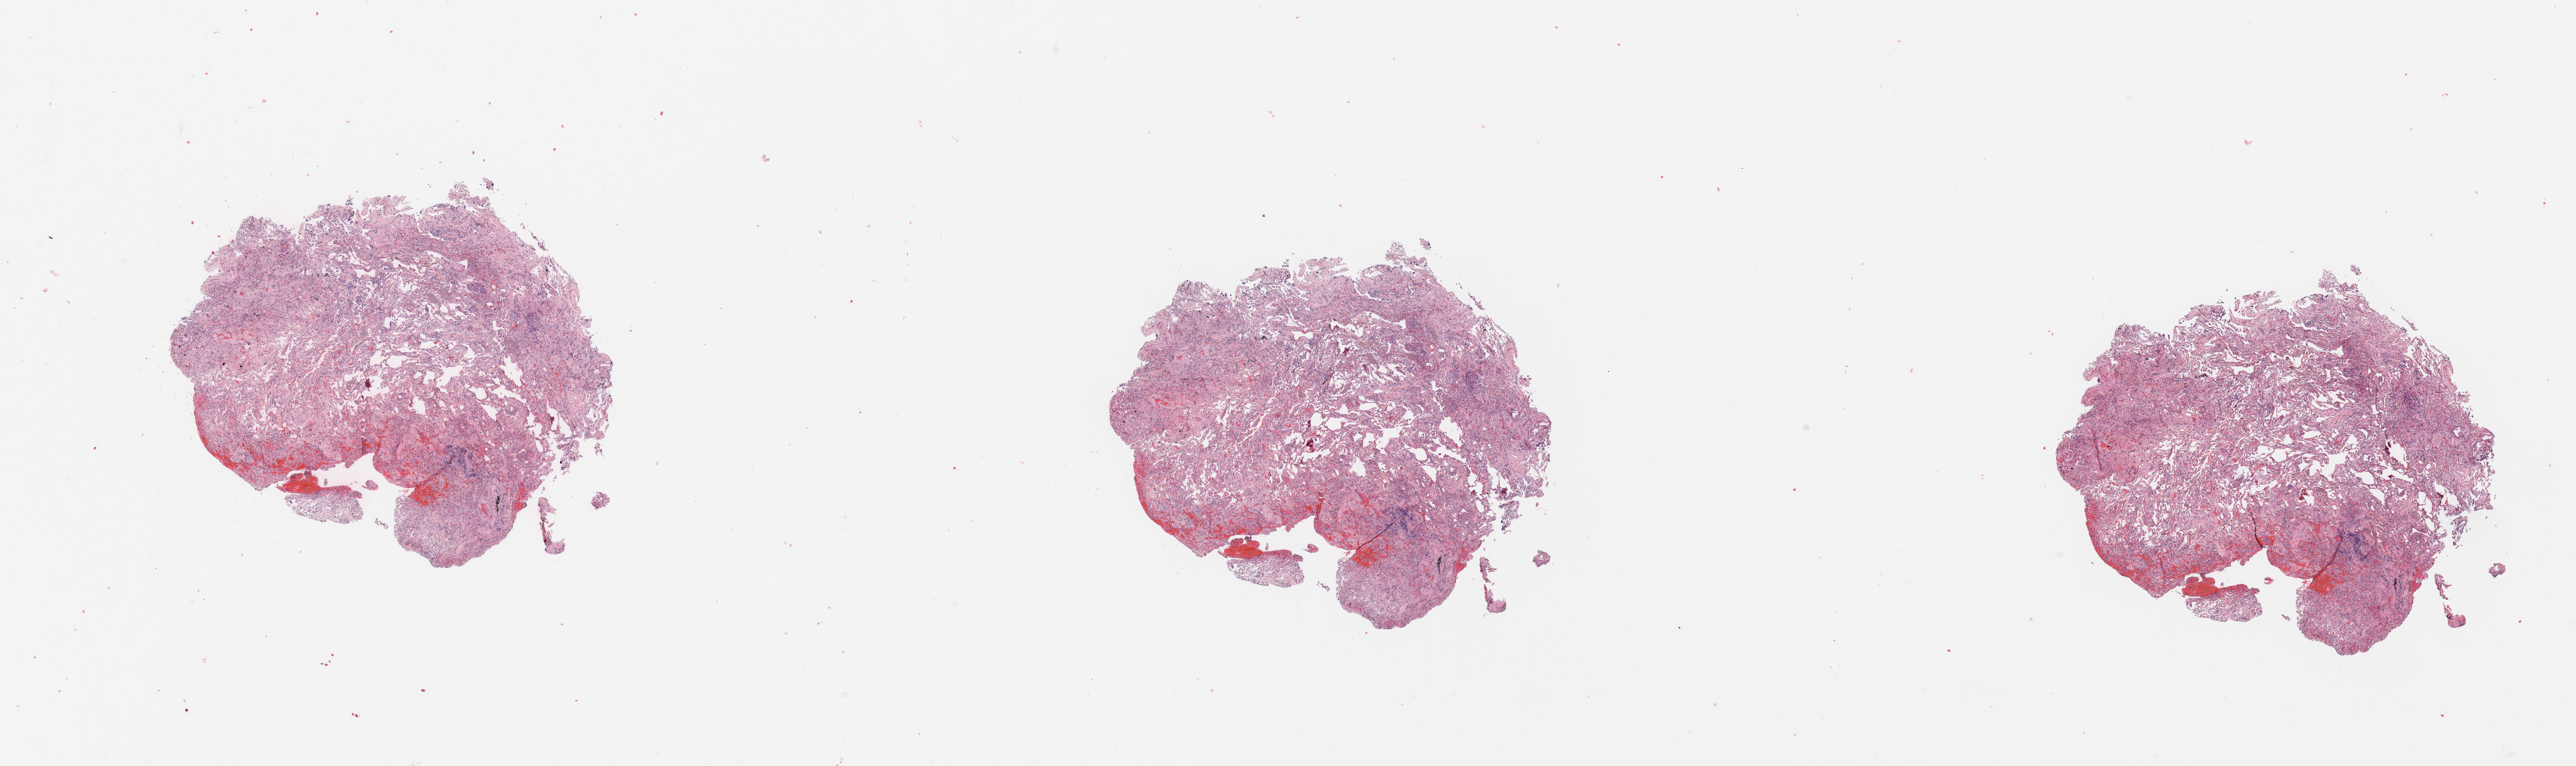
Hematoxylin and eosin (H&E) stained whole-slide image — shown as a low-resolution overview of the whole scanned area (about 30.5 x 9.1 mm). Lung, normal (non-tumour) tissue. 68-year-old female patient.
- this section: normal (non-tumour) tissue from the same patient
- patient diagnosis: Adenocarcinoma, NOS